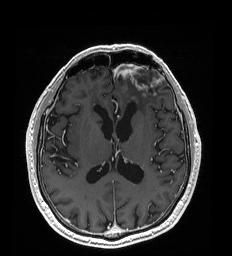
Brain MRI from a brain-tumour surgery series, one axial slice; slice 96 of 192 in the series (ordered by position); T1-weighted post-contrast; 1 mm slice thickness; 232 × 256 image matrix, field of view 227 × 250 mm. Case-level facts recorded for this patient, not image findings: histopathology: Glioblastoma; WHO grade: 4; IDH mutation: no.
Annotated regions visible in this slice (expert manual segmentation):
- tumour: box from (x=131, y=98) to (x=135, y=100) px